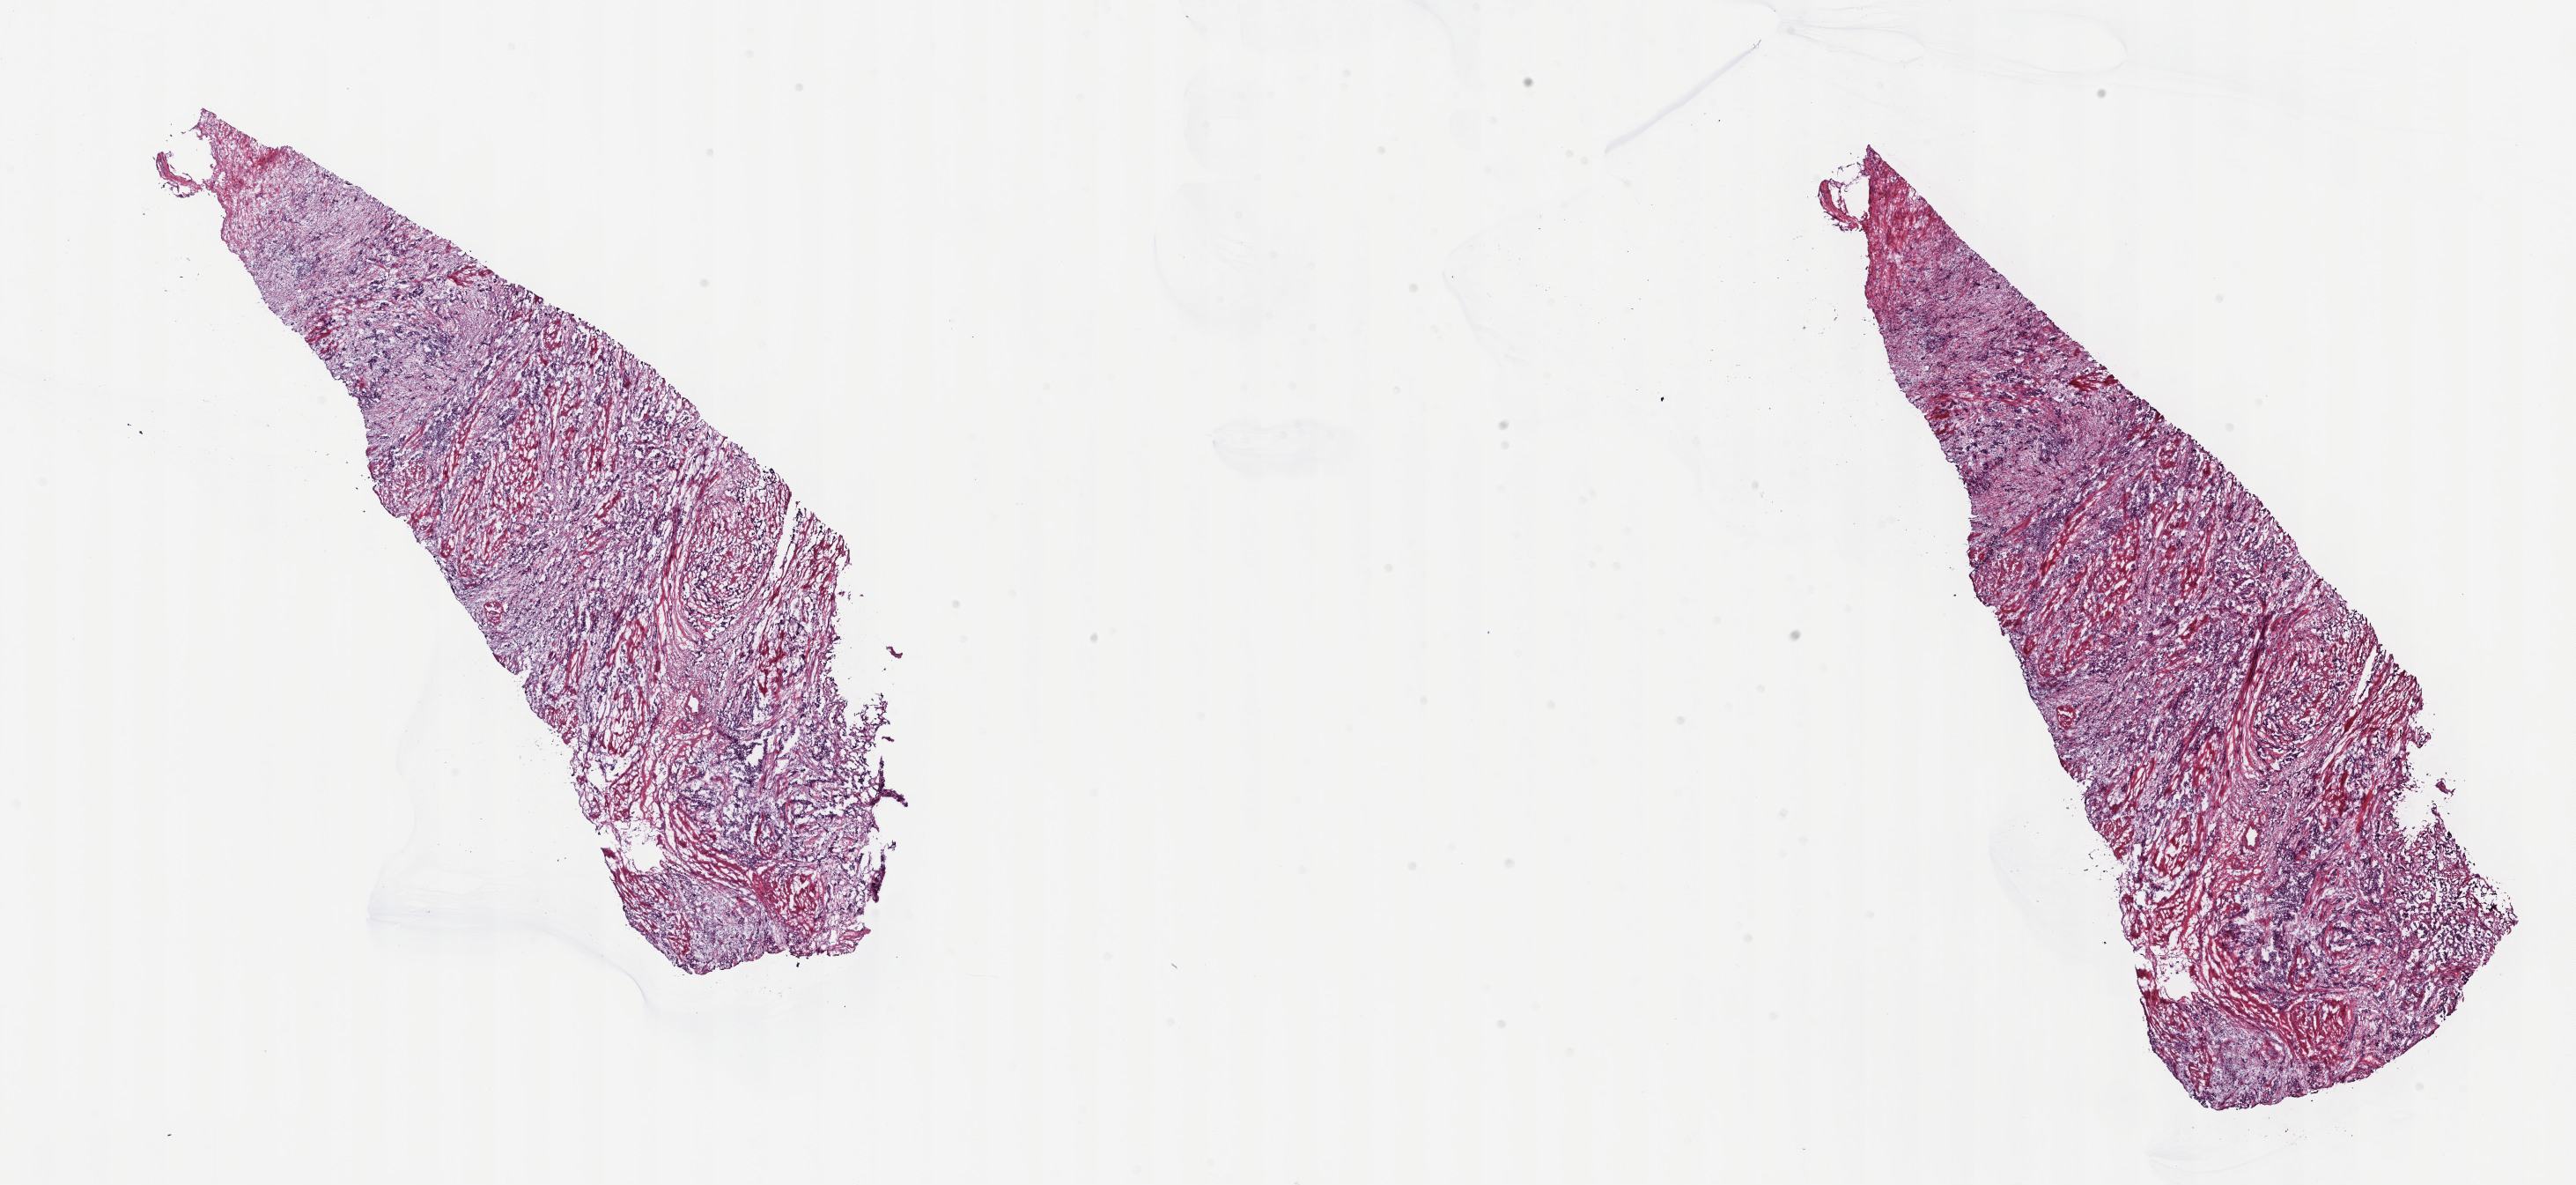
Whole-slide histology image, H&E-stained — whole scanned area (about 23.7 x 10.9 mm) shown as a low-resolution overview; frozen section; primary tumour sample from the bladder. Patient: male, age at initial diagnosis 60 years. Histologic grade: high grade. Pathologist review of this section (percent, as recorded): tumour cells 100%, tumour nuclei 65%, normal cells 0%, stromal cells 0%, necrosis 0%. Inflammatory infiltration, as recorded: lymphocyte infiltration 2%, monocyte infiltration 0%, neutrophil infiltration 0%.
* AJCC pathologic stage: III
* lymph nodes positive (case pathology): 0 of 19 examined
* pathologic diagnosis: Transitional cell carcinoma (lateral wall of bladder)